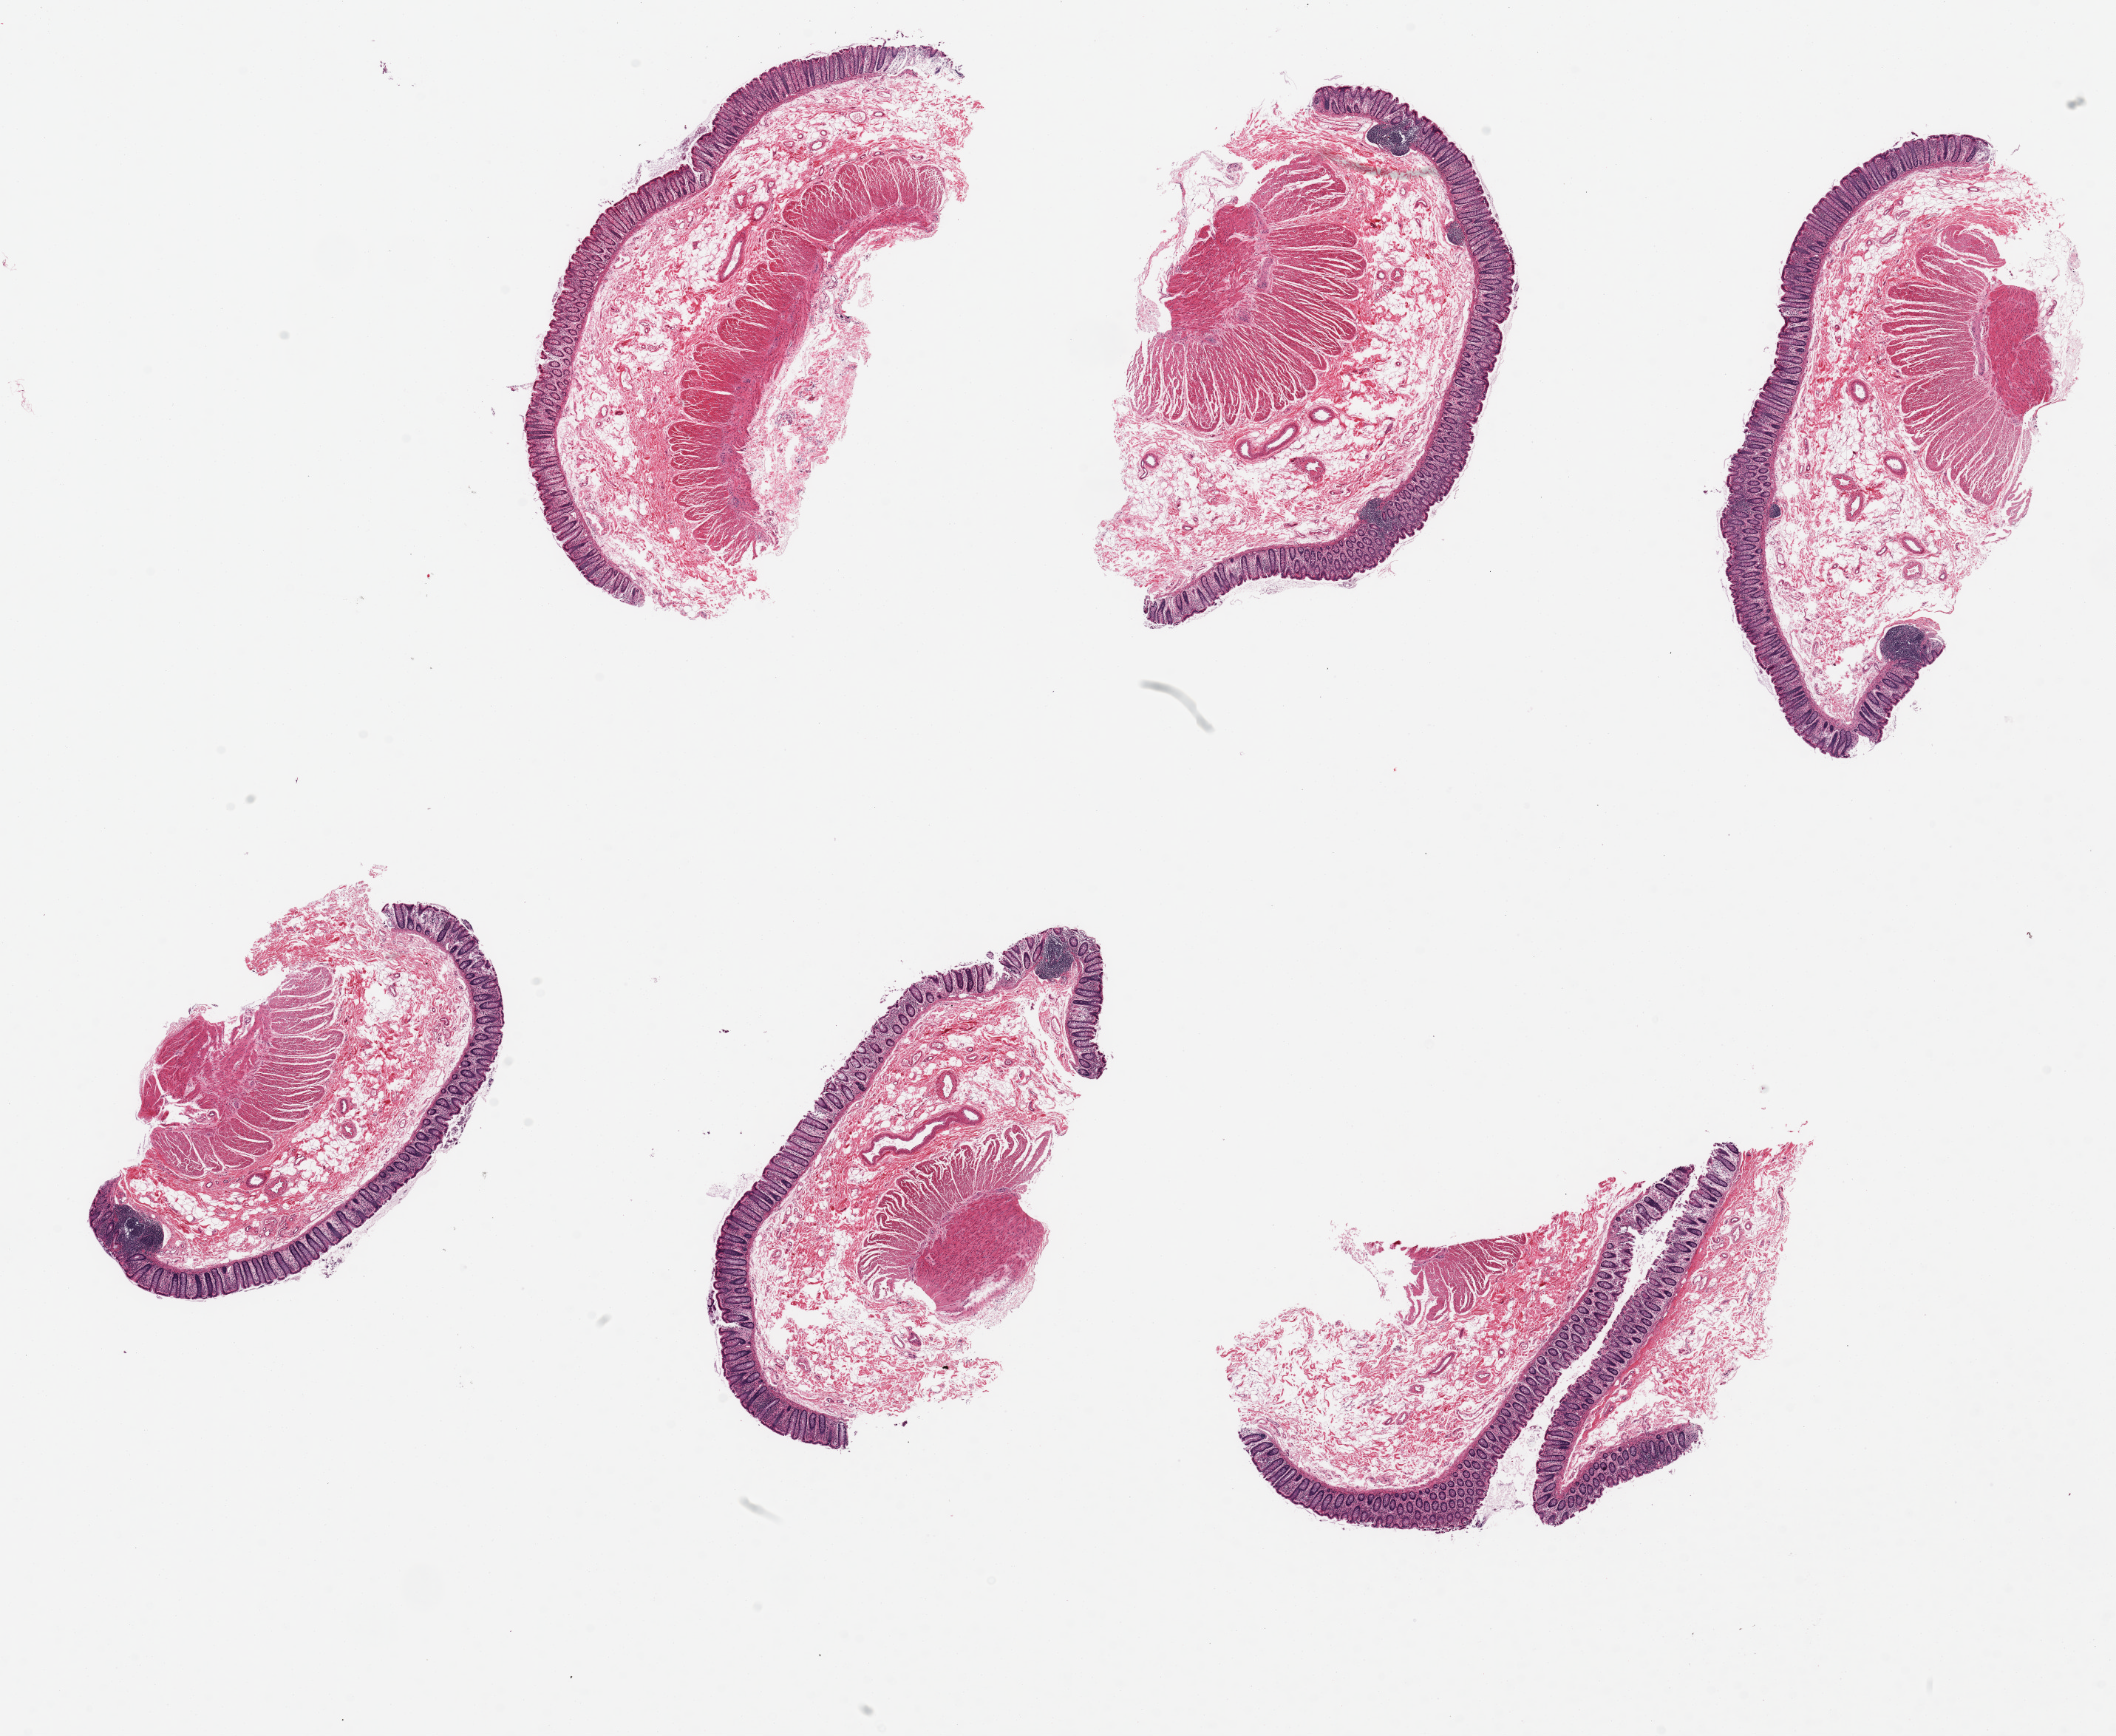
Digitized haematoxylin and eosin-stained section — a low-resolution overview of the entire scanned area, about 22.6 x 18.6 mm; PAXgene-fixed paraffin-embedded (PFPE) section; target tissue: transverse colon; tissue donor sample.
Review note (as recorded): 6 pieces up to 7x3 mm; good mucosal preservation.